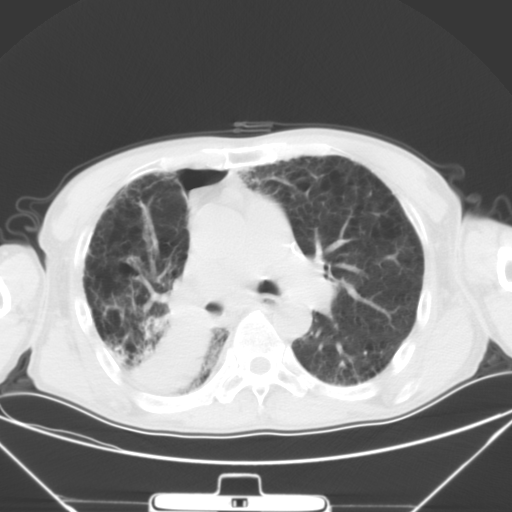
Chest CT, one axial slice; position 28 of 50 along the scan axis; lung window (W 1500 / L -600 HU); 5 mm slice thickness; 512 × 512 image matrix, field of view 373 × 373 mm. Male patient, age 65 years. From the clinical record (not read from this slice): clinical TNM (as recorded): T3 N1 M1a.
Structures marked on this image (rectangle marked by the reading radiologist):
- lung tumour (recorded histology: squamous cell carcinoma): bounding box <129,283,207,406> (left, top, right, bottom; pixels)